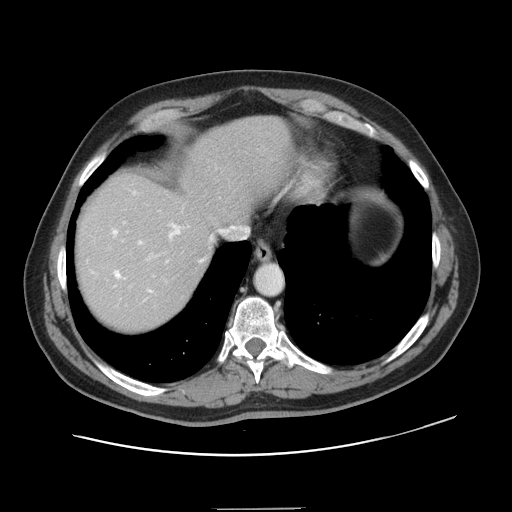
Contrast-enhanced abdominal CT, one axial slice; slice 124 of 143 in the series (ordered by position); 120 kVp; intravenous contrast given; soft-tissue window (W 400 / L 40 HU); 2.5 mm slice thickness; 512 × 512 image matrix, field of view 402 × 402 mm. Male patient, age 62 years. Case-level facts recorded for this patient, not image findings: diagnosis: colorectal cancer liver metastases, imaged before liver resection; multiple liver metastases: yes; largest metastasis: 2.7 cm.
Annotated regions visible in this slice (outlined manually by an expert reader):
- hepatic veins: bounding box <112,192,202,292> (left, top, right, bottom; pixels)
- liver: <76,116,291,332>
- planned liver remnant (the part of the liver to remain after resection): <76,116,290,295>
- portal vein (with intrahepatic branches): <122,222,151,260>